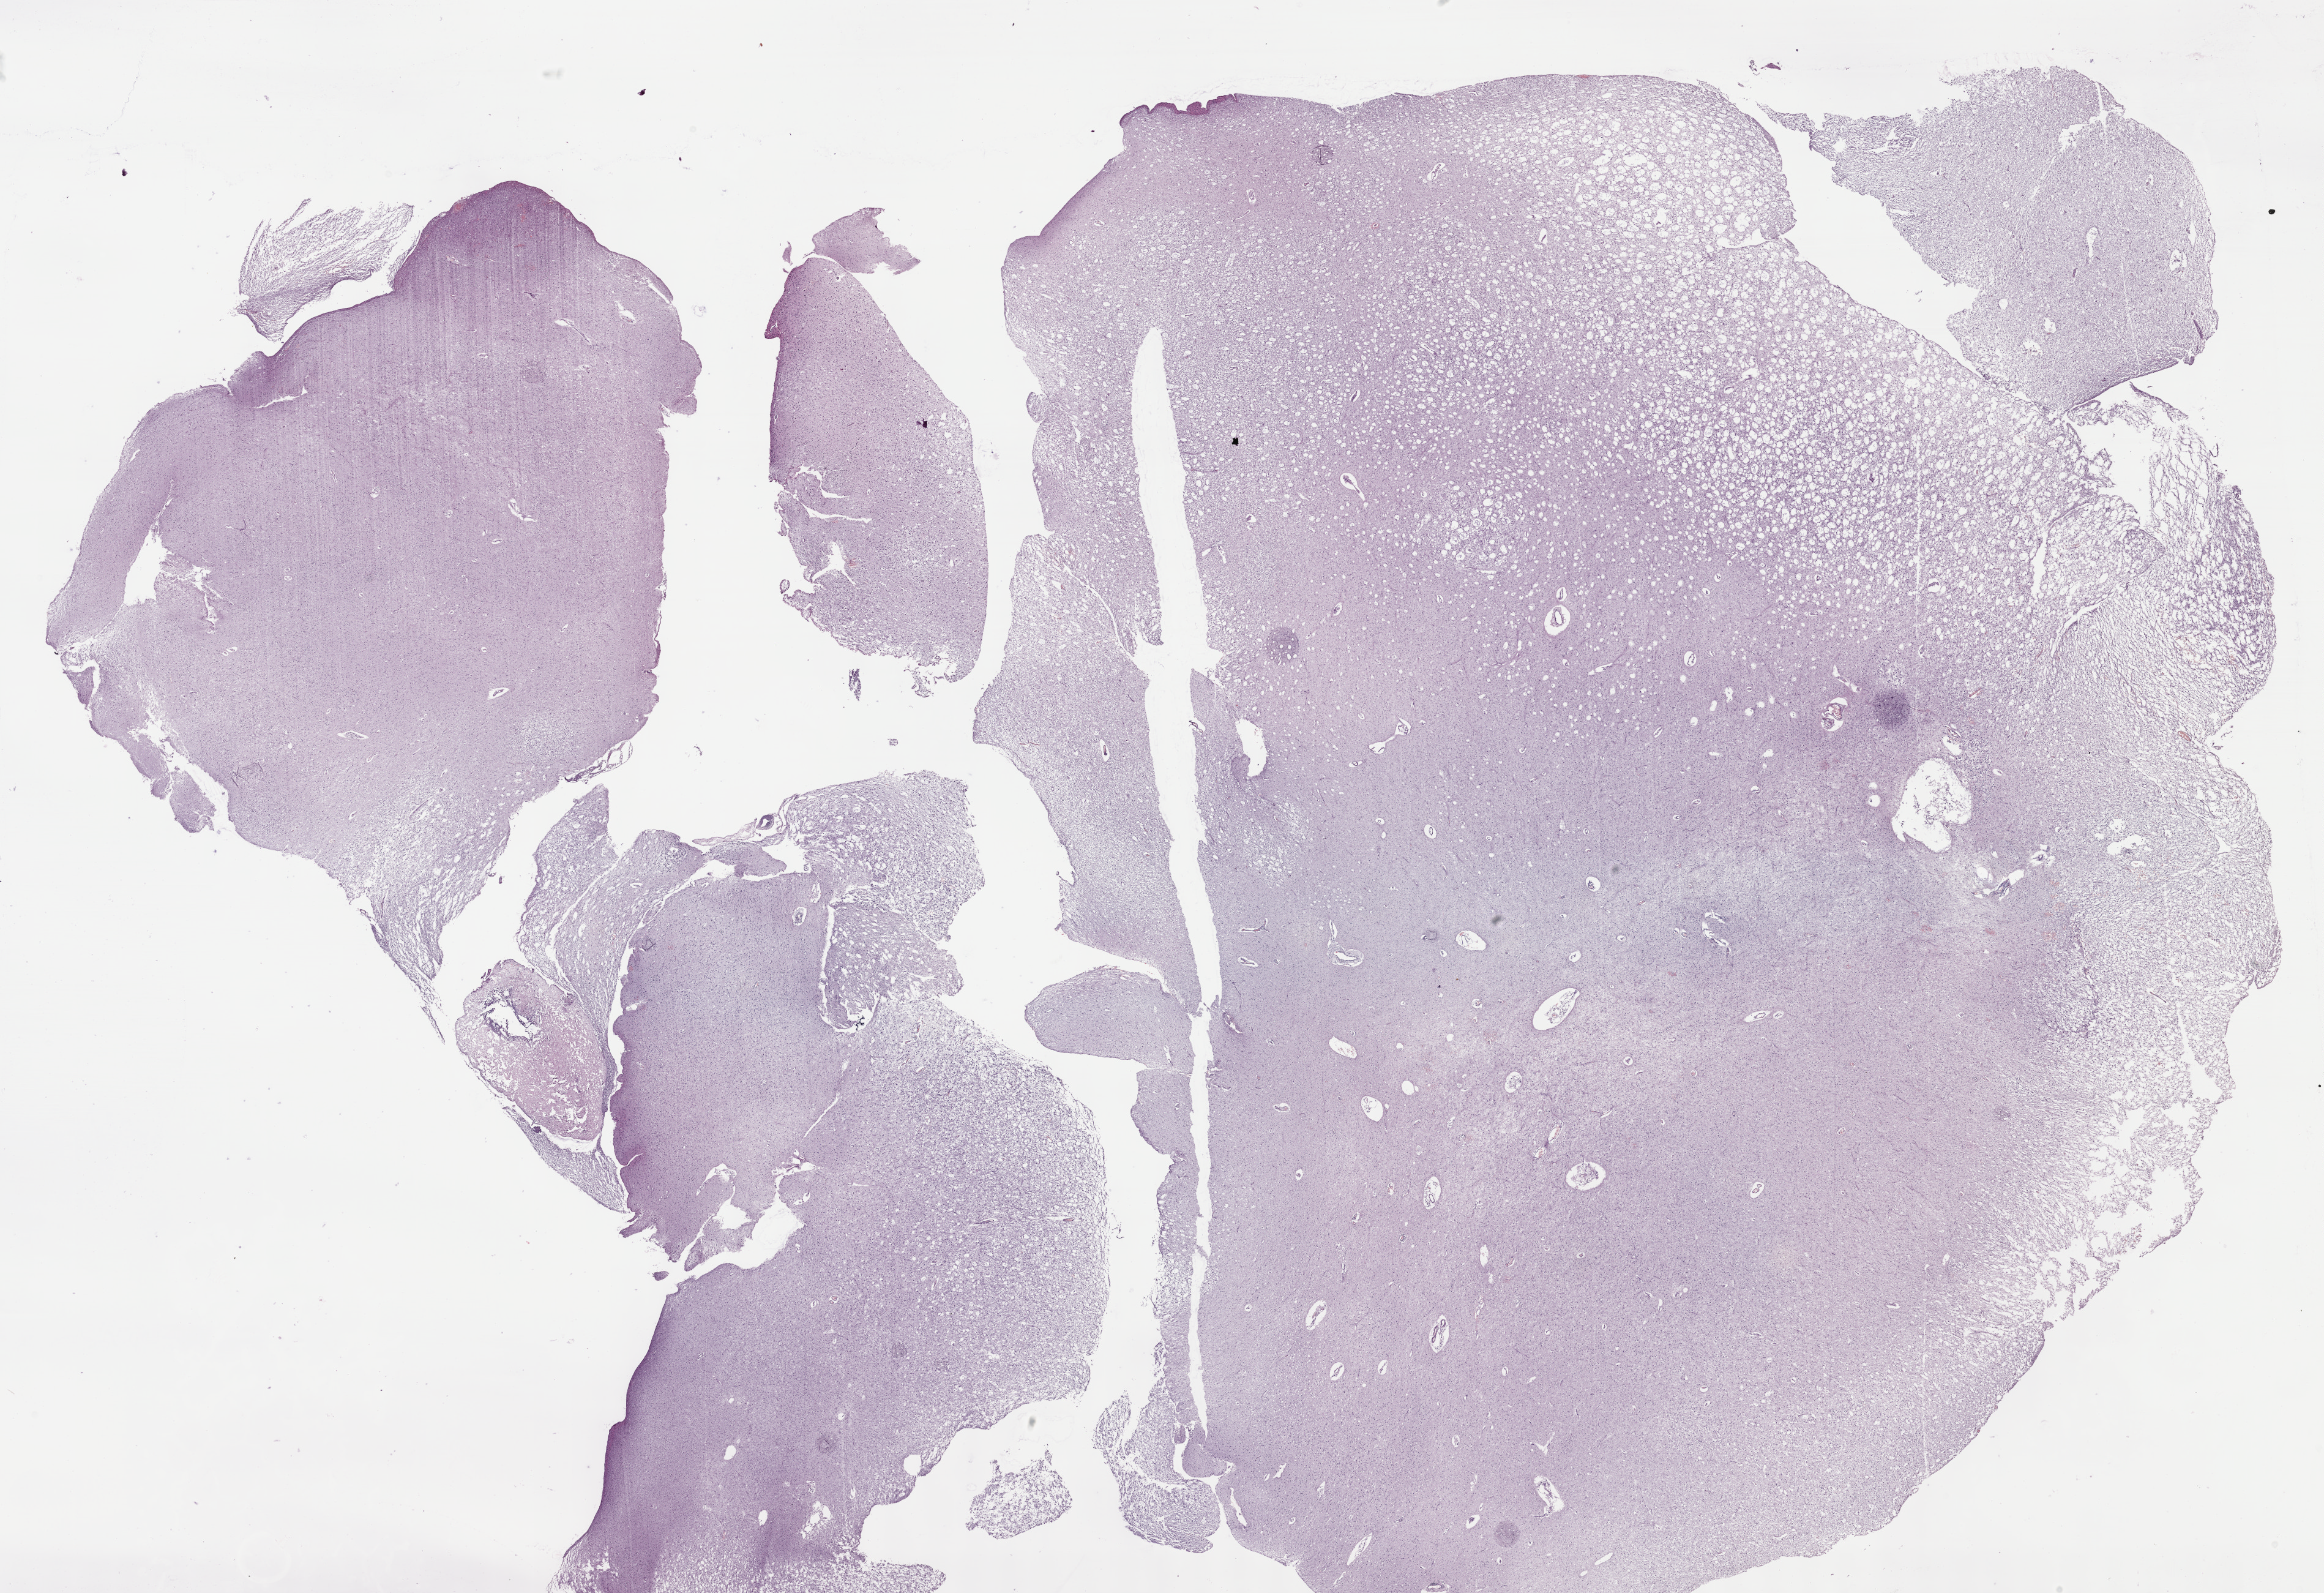
Digitized H&E-stained tissue section (whole slide), low-resolution overview of the scanned area, about 30.7 x 21.0 mm (acquisition: 40x scan); formalin-fixed paraffin-embedded (FFPE) diagnostic section; primary tumour sample from the brain. Male, age 47 years at initial diagnosis. Histologic grade: G2 (moderately differentiated).
Pathologic diagnosis: Astrocytoma, NOS (cerebrum).